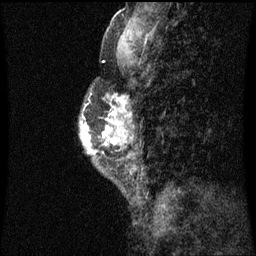
Breast MRI (dynamic contrast-enhanced), one sagittal slice; position 20 of 60 along the scan axis; dynamic contrast-enhanced series, image 2 of 3 at this slice position (ordered by acquisition); 1.5 T; TE 4.2 ms, TR 8.9 ms; 2 mm slice thickness; 256 × 256 image matrix, field of view 200 × 200 mm. Patient: female, 50 years. Case-level facts recorded for this patient, not image findings: setting: breast cancer imaged before/during neoadjuvant chemotherapy; receptor status: triple-negative.
Structures marked on this image (semi-automatically segmented with operator editing):
- analysis volume of interest (the breast-tissue region the enhancement analysis was run in; not a lesion): box from (x=80, y=92) to (x=116, y=169) px
- tumour enhancement mask (voxels above the 70 % enhancement threshold inside the analysis volume of interest): (x=87, y=112)–(x=116, y=131)